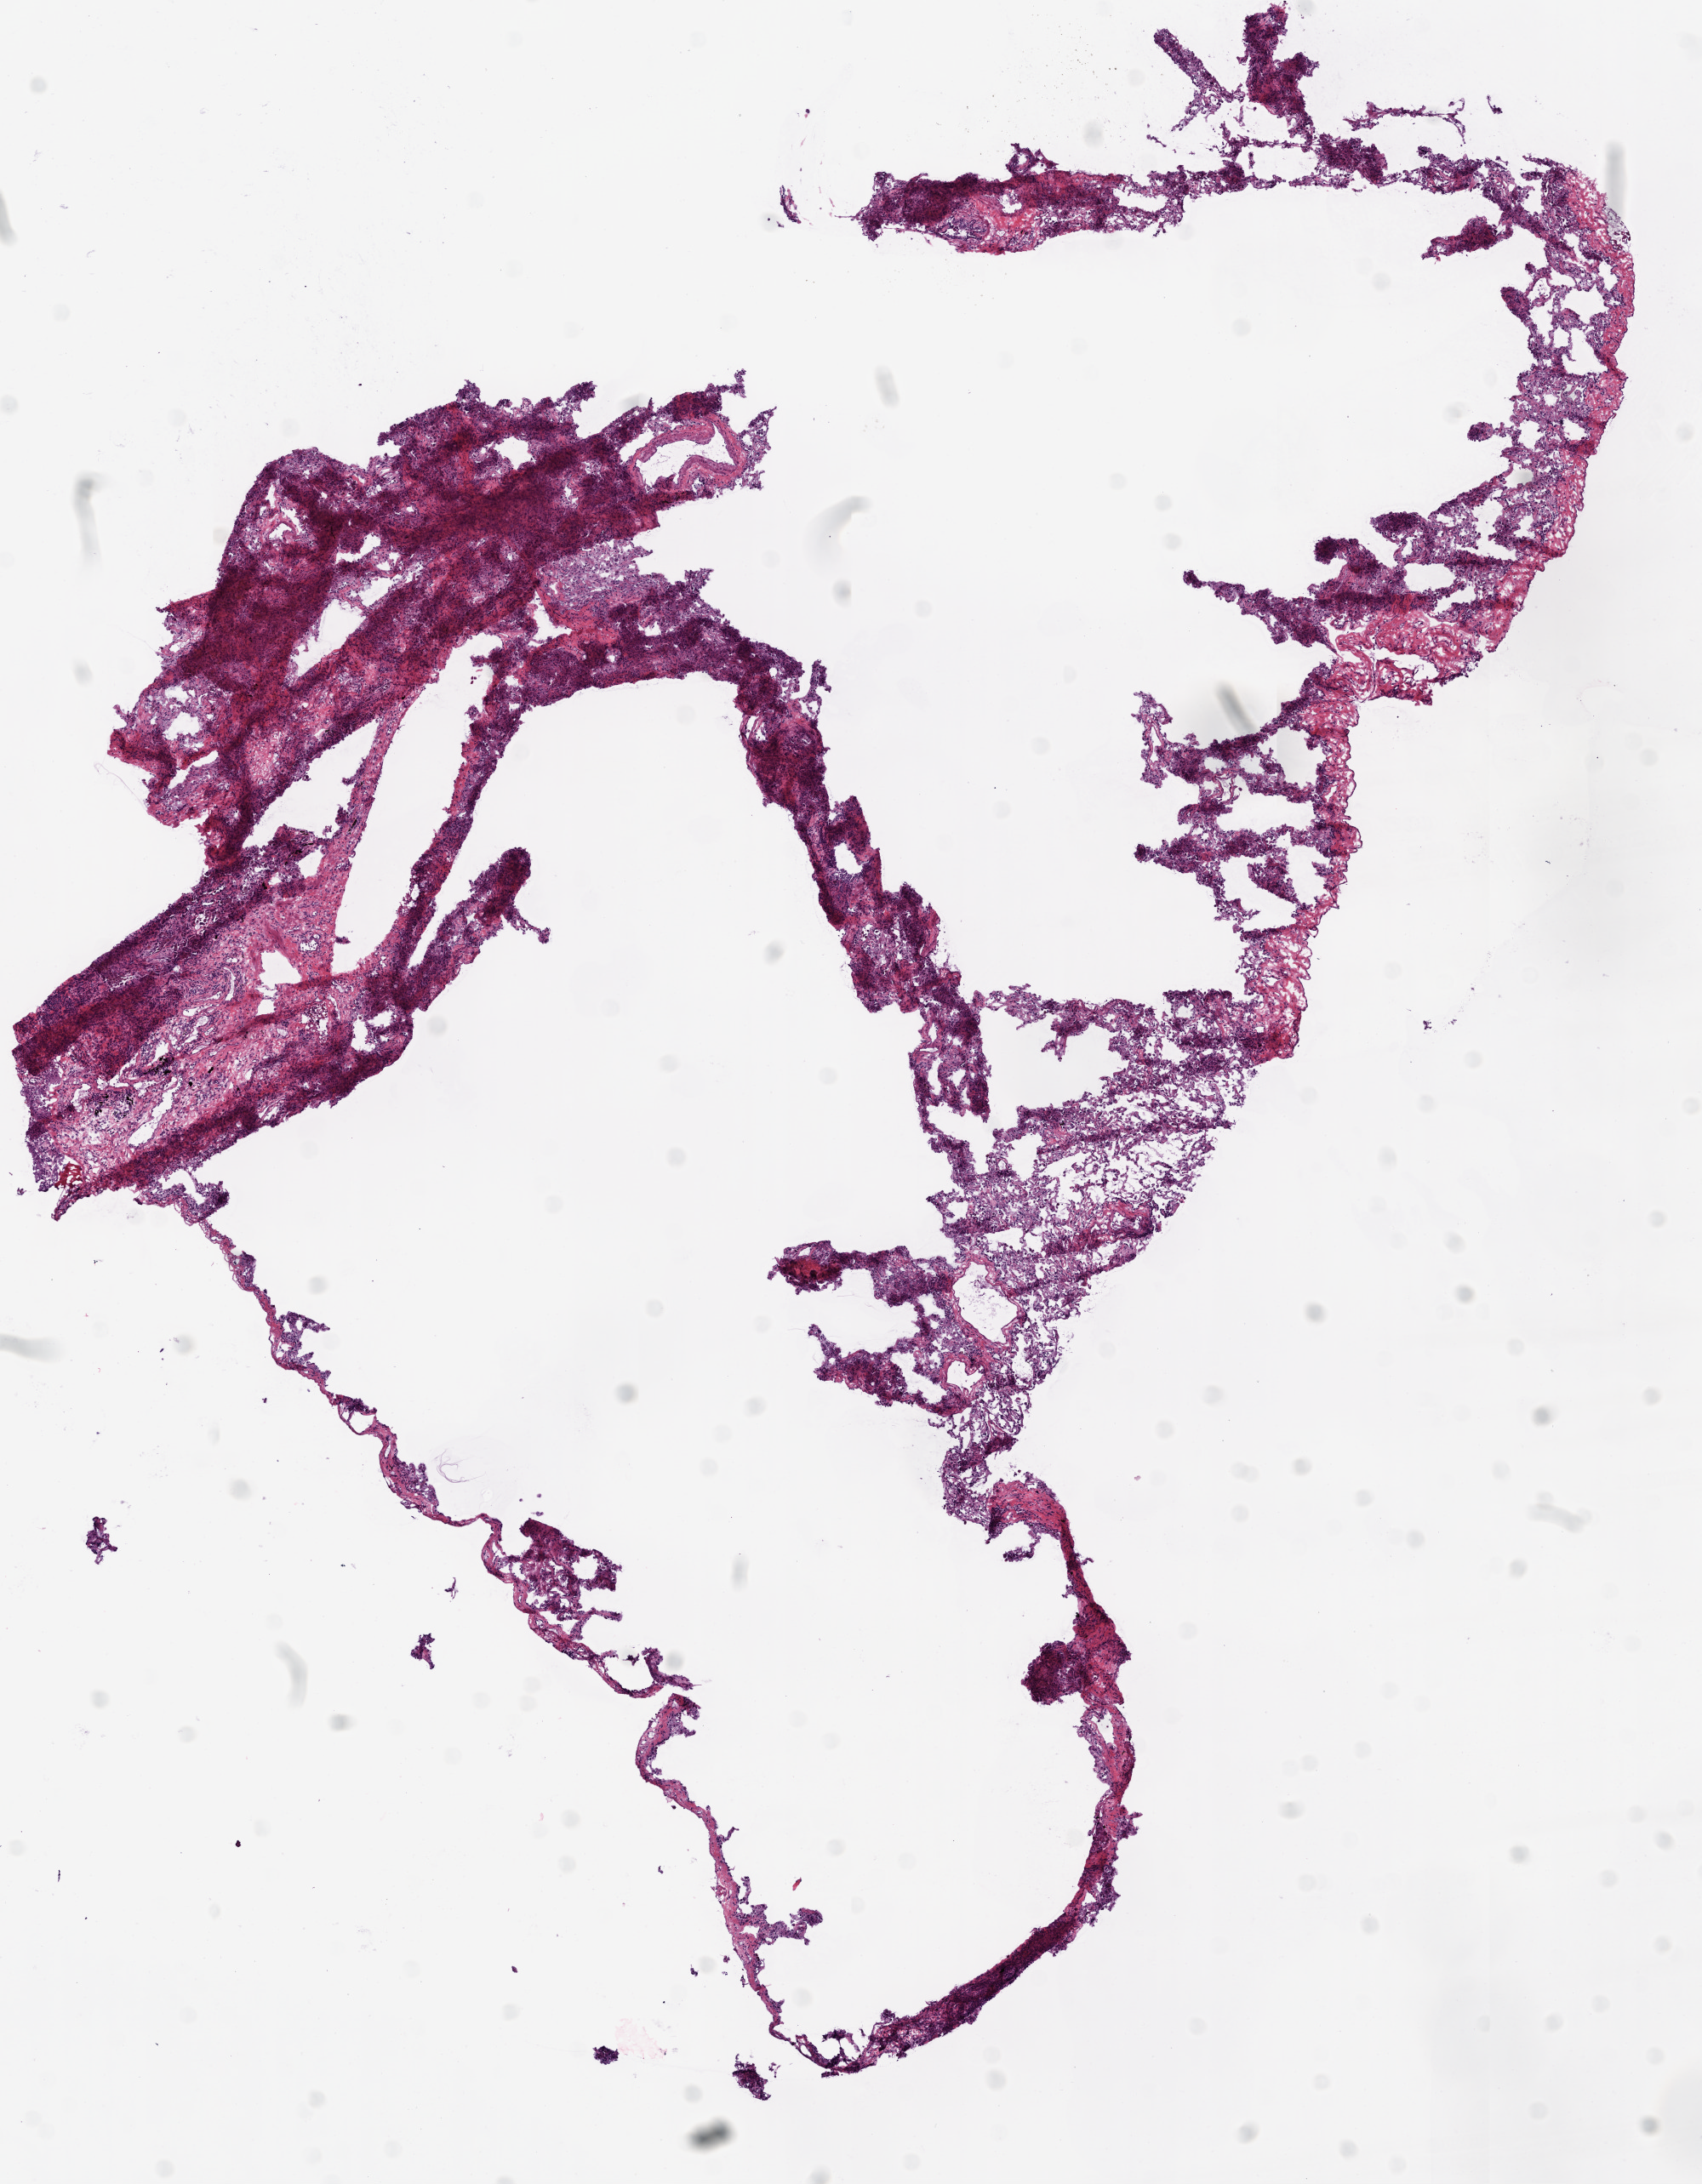
Digitized H&E-stained tissue section (whole slide) — shown as a low-resolution overview of the whole scanned area (about 8.0 x 10.3 mm, slide scanned at 20x). Frozen section from the top of the tissue portion. Lung, solid tissue normal (non-tumour tissue) sample. Male patient; age at initial diagnosis 71 years.
This section: solid tissue normal (non-tumour) sample from the same patient. Patient diagnosis: Squamous cell carcinoma, NOS.